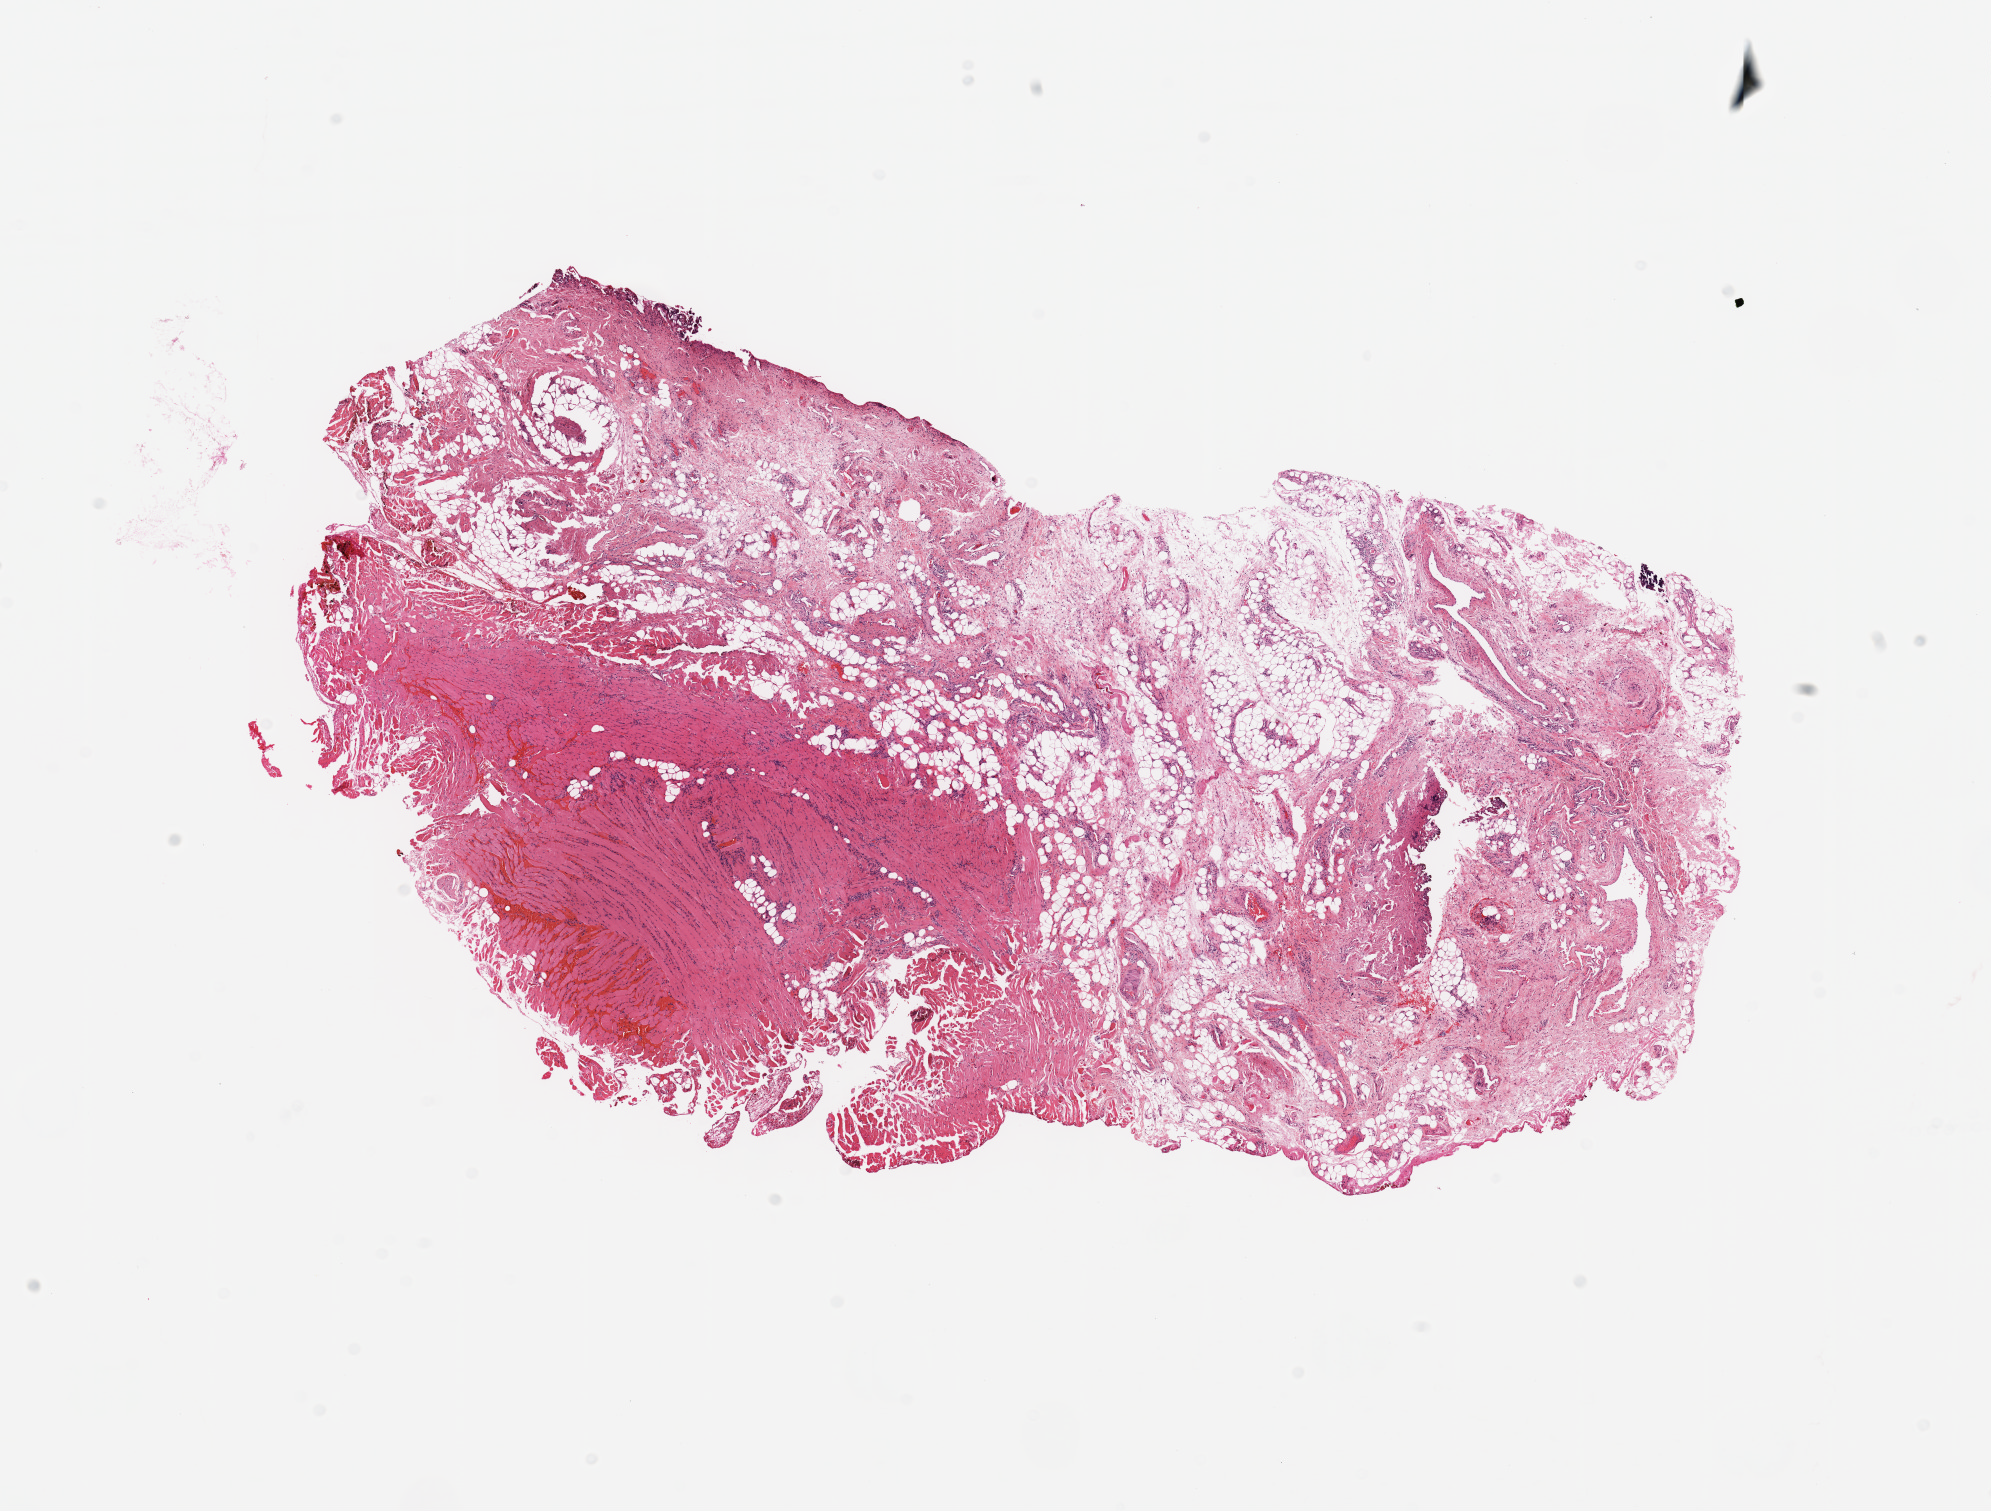
H&E whole-slide image, shown as a low-resolution overview of the whole scanned area (about 15.8 x 12.0 mm, slide scanned at 20x), normal (non-tumour) tissue sample, sampled site: oral cavity. Patient: male, age 56 years.
• this section: normal (non-tumour) tissue from the same patient
• patient diagnosis: Squamous cell carcinoma, NOS (overlapping lesion of lip, oral cavity and pharynx)